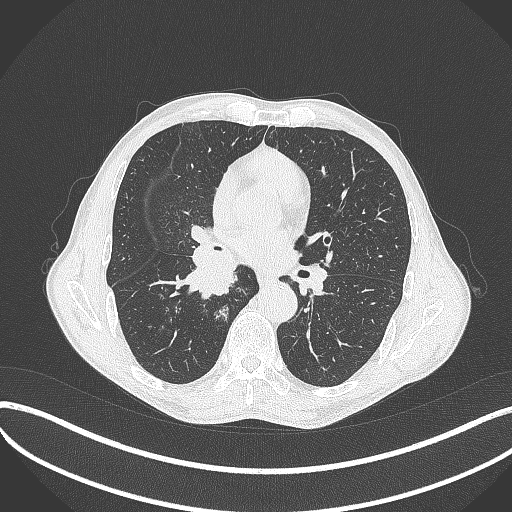
Chest CT, one axial slice. Position 222 of 481 along the scan axis. Reconstruction kernel B70f. 120 kVp. Lung window (W 1500 / L -600 HU). 512 × 512 image matrix. Patient: male, 65 years. Case-level facts recorded for this patient, not image findings: clinical TNM (as recorded): T2a N0 M0; histopathological grade: G2.
Annotated regions visible in this slice (rectangle marked by the reading radiologist):
- lung tumour (recorded histology: squamous cell carcinoma): box from (x=183, y=232) to (x=241, y=301) px